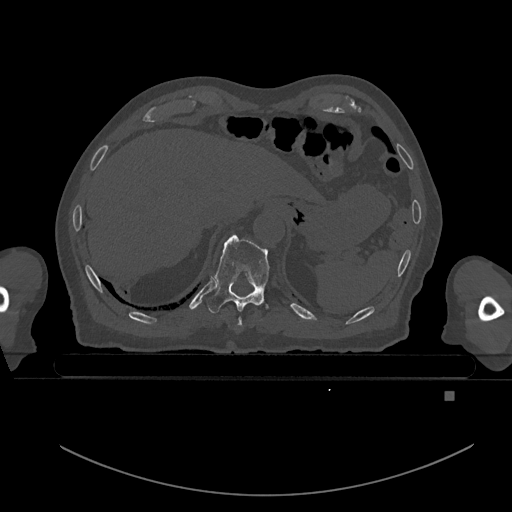
CT including the spine, one axial slice; slice 91 of 969 in the series (ordered by position); bone window (W 1800 / L 400 HU); 512 × 512 image matrix. Patient: male, 82 years. From the clinical record (not read from this slice): primary cancer: prostate; vertebrae with lytic lesions (as recorded): T11, T9, T8, T2.
Structures marked on this image (semi-automatic segmentation, software-assisted and operator-edited):
- T10 vertebra: bounding box <207,234,271,314> (left, top, right, bottom; pixels)
- T9 vertebra: <238,317,243,328>